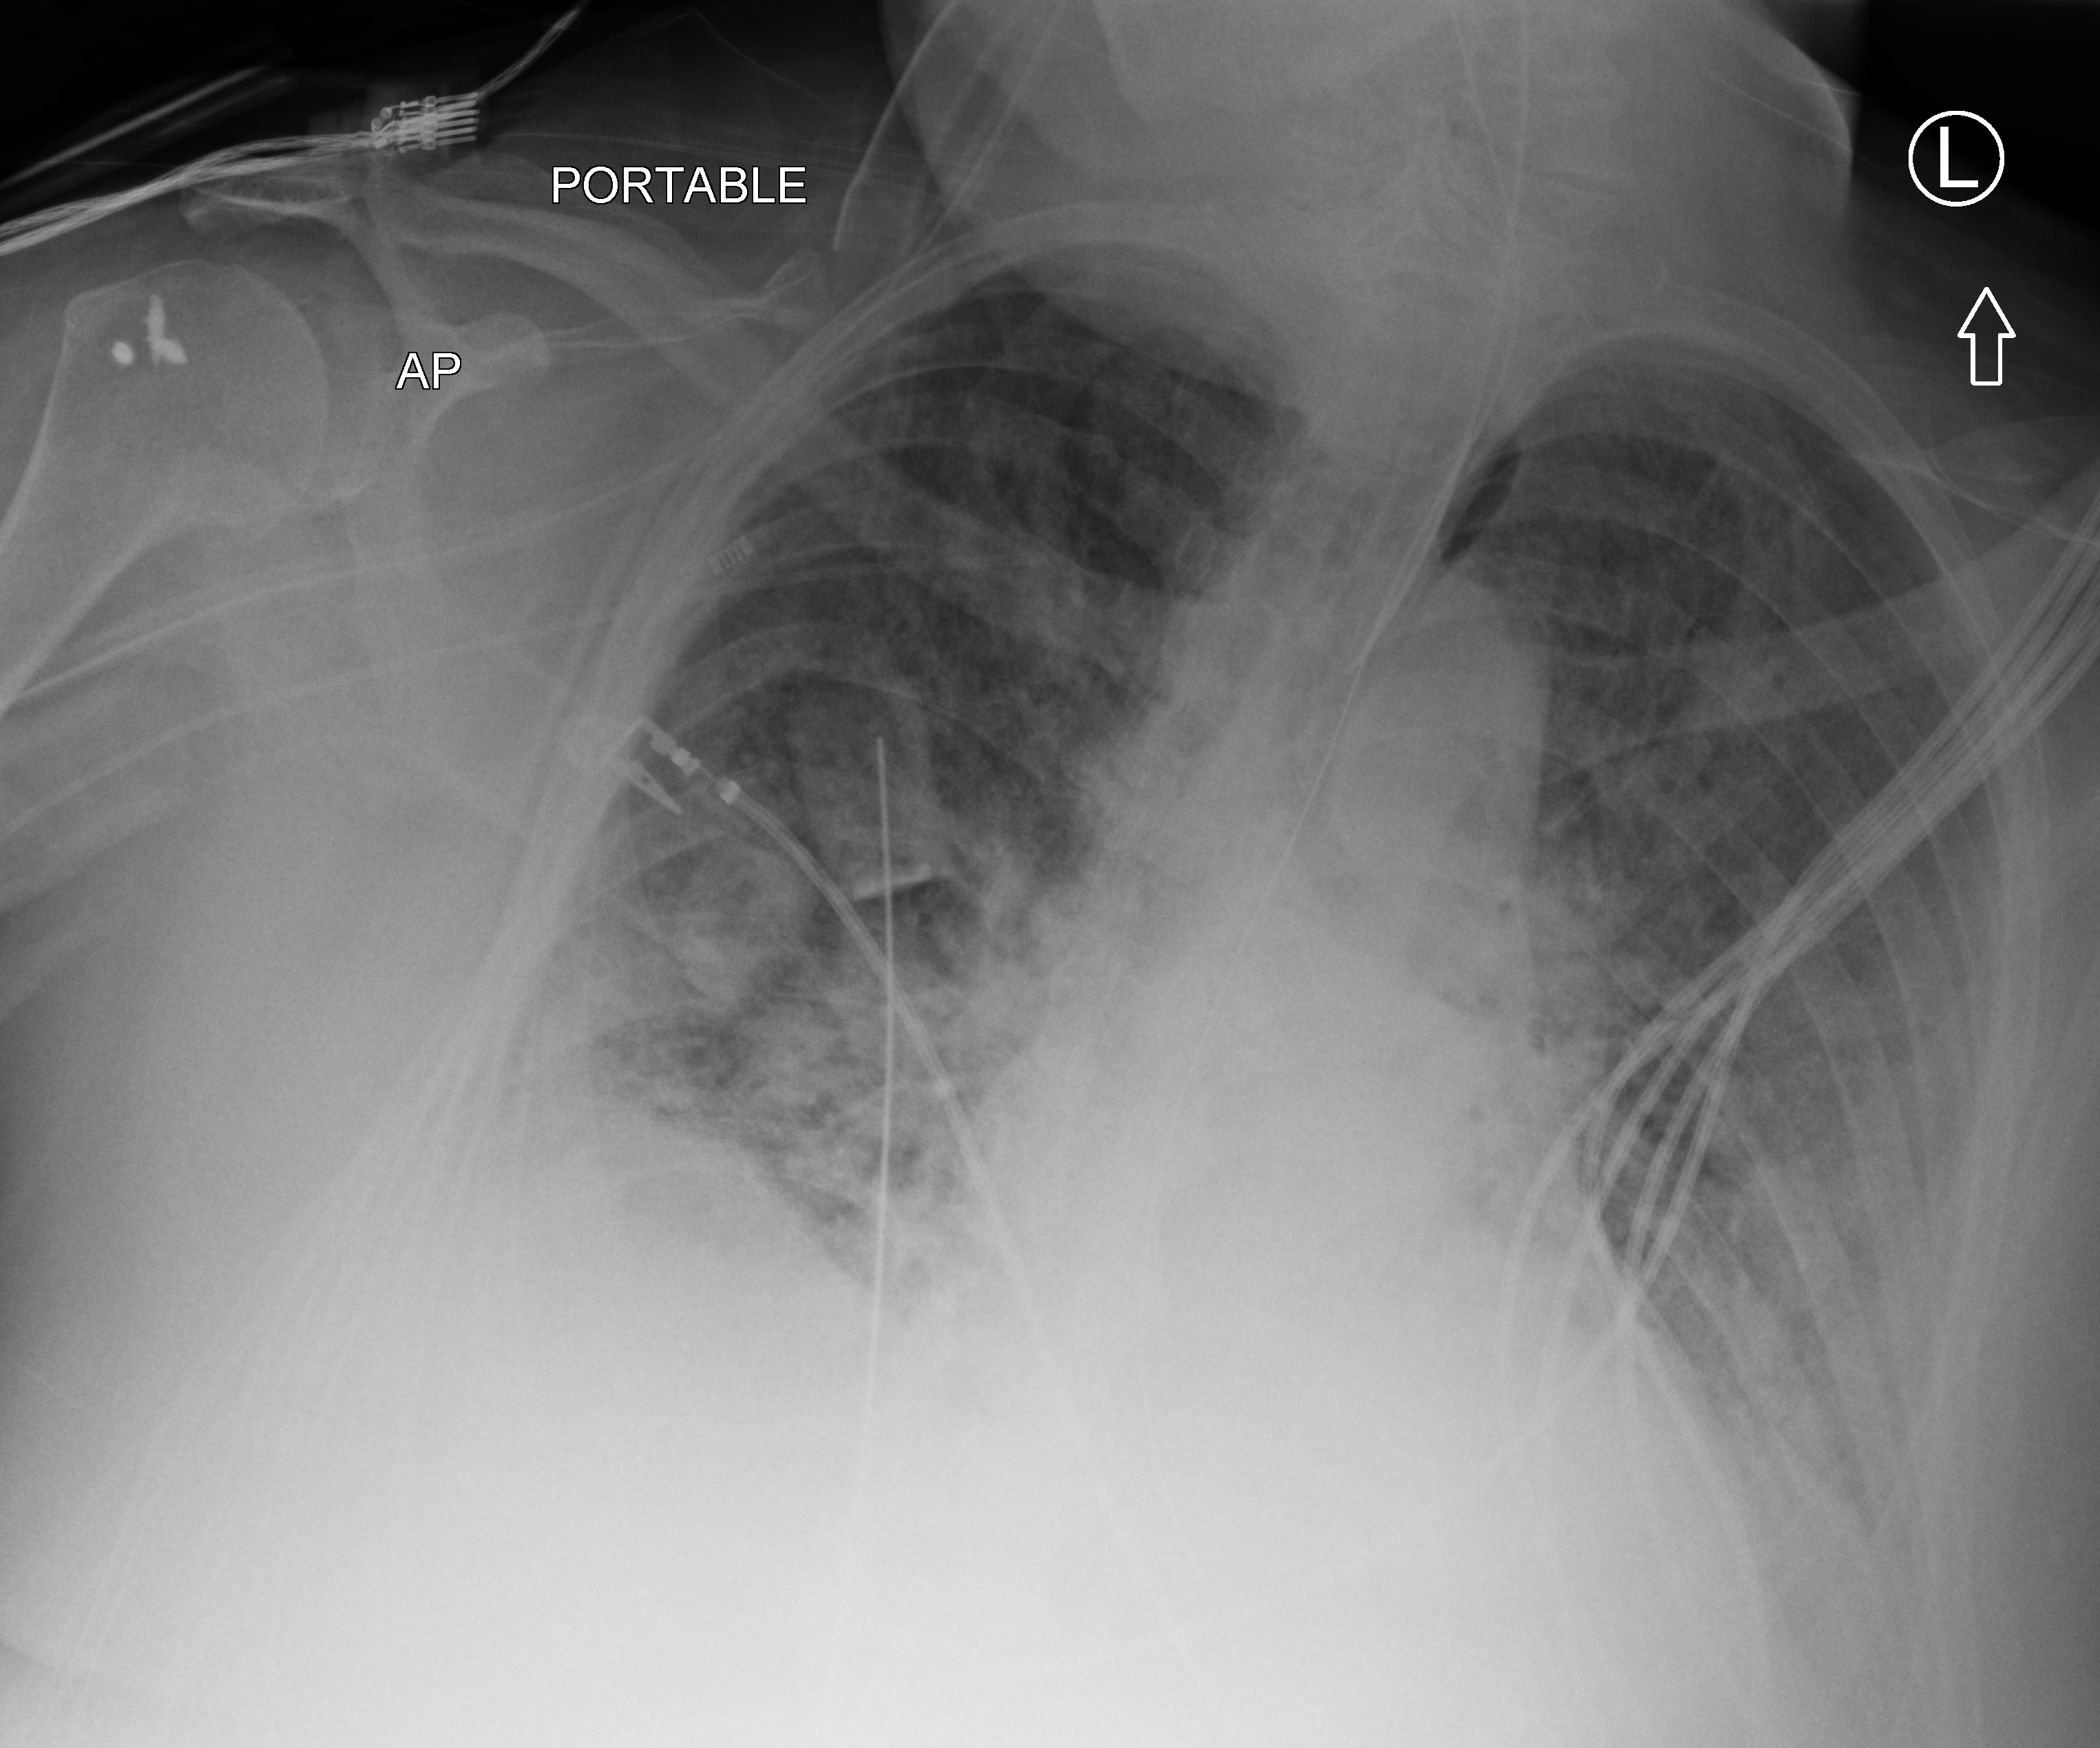
Bedside chest radiograph (computed radiography), anteroposterior (AP) projection. Patient hospitalised with COVID-19; male, aged 60–74 years.
Admission-level facts for this patient (not findings on this image; timing relative to this image not recorded):
- admitted to intensive care during this hospital stay: yes